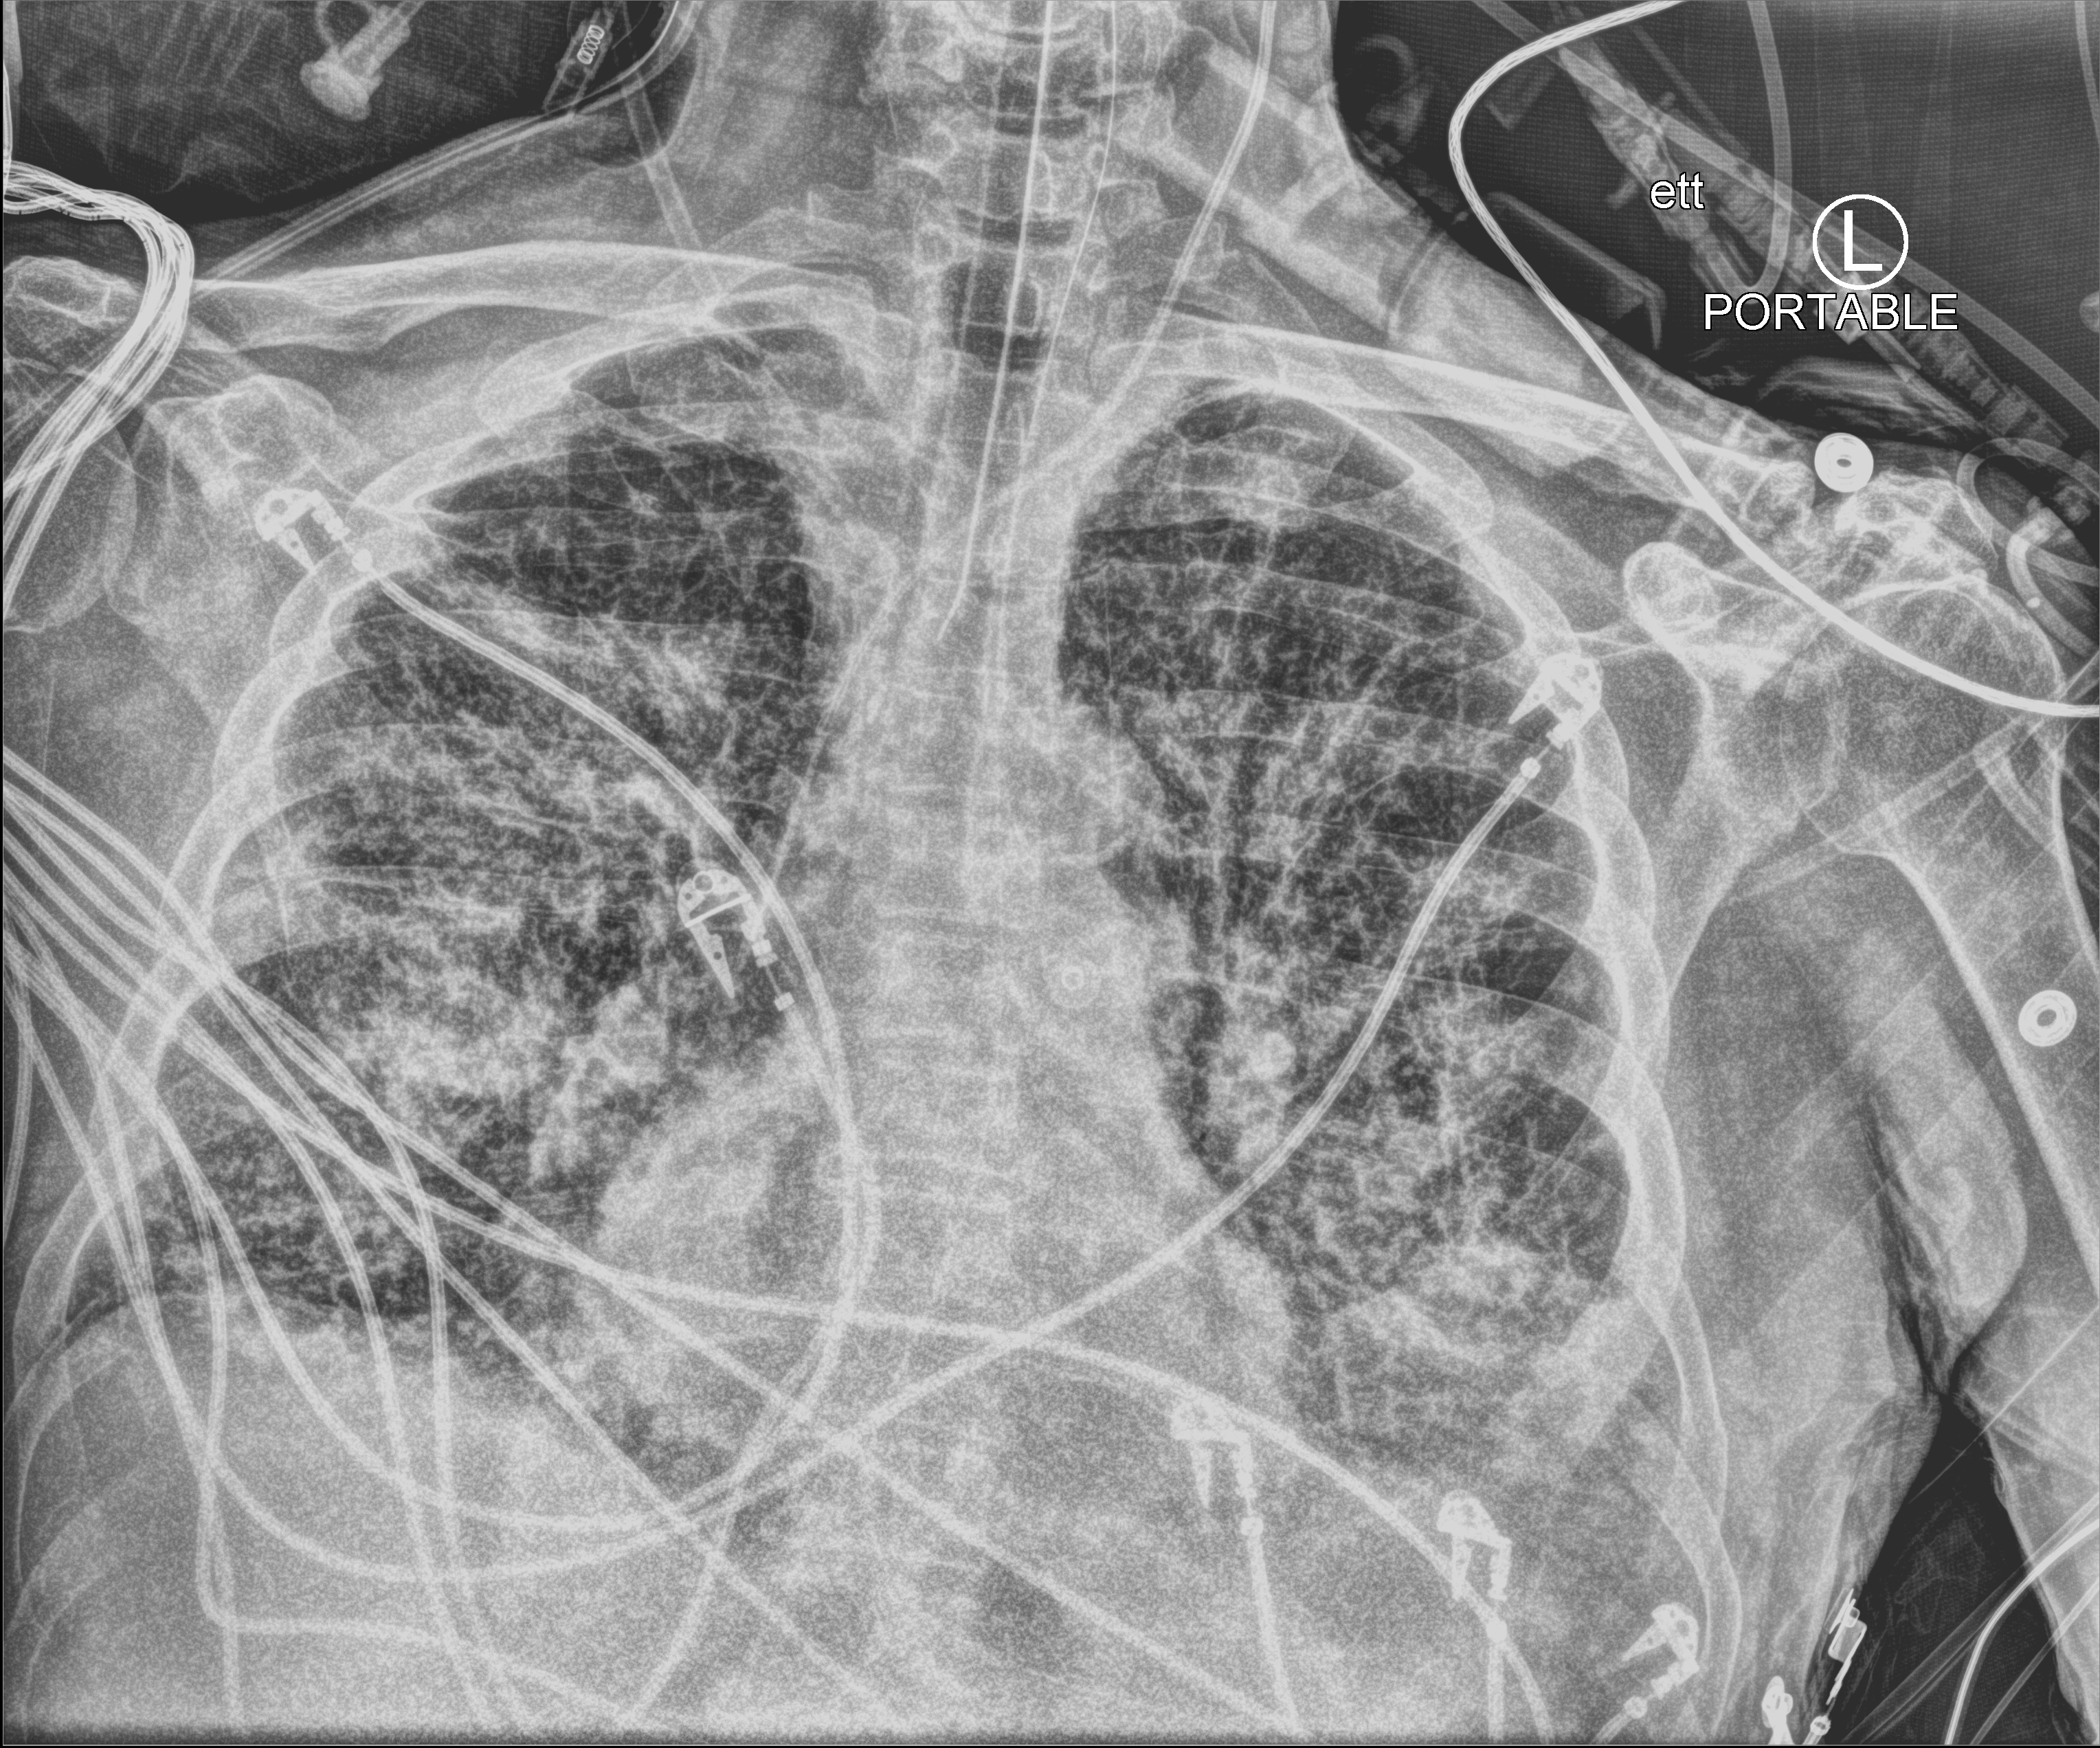
Bedside chest radiograph (computed radiography), anteroposterior (AP) projection. Patient hospitalised with COVID-19; male, aged 75–90 years.
Admission-level facts for this patient (not findings on this image; timing relative to this image not recorded): admitted to intensive care during this hospital stay: yes.